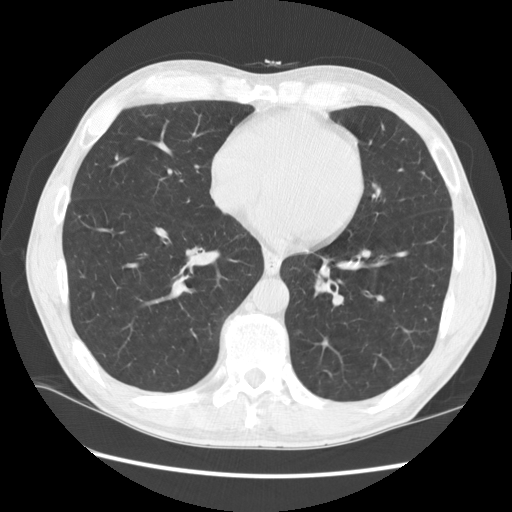
Chest CT (low-dose screening protocol), one axial image, baseline annual screen, lung window (W 1500 / L -600 HU), standard (soft-tissue) reconstruction kernel (STANDARD), 120 kVp, slice 92 of 141 in the series. Male participant, aged 57 years at enrolment. Current smoker at enrolment.
Expert-annotated lung lesion, box from (x=267, y=249) to (x=346, y=317) px. The screening reader recorded 2 non-calcified nodules or masses ≥4 mm on this exam (left lower lobe, lingula); which of them this box marks is not recorded.